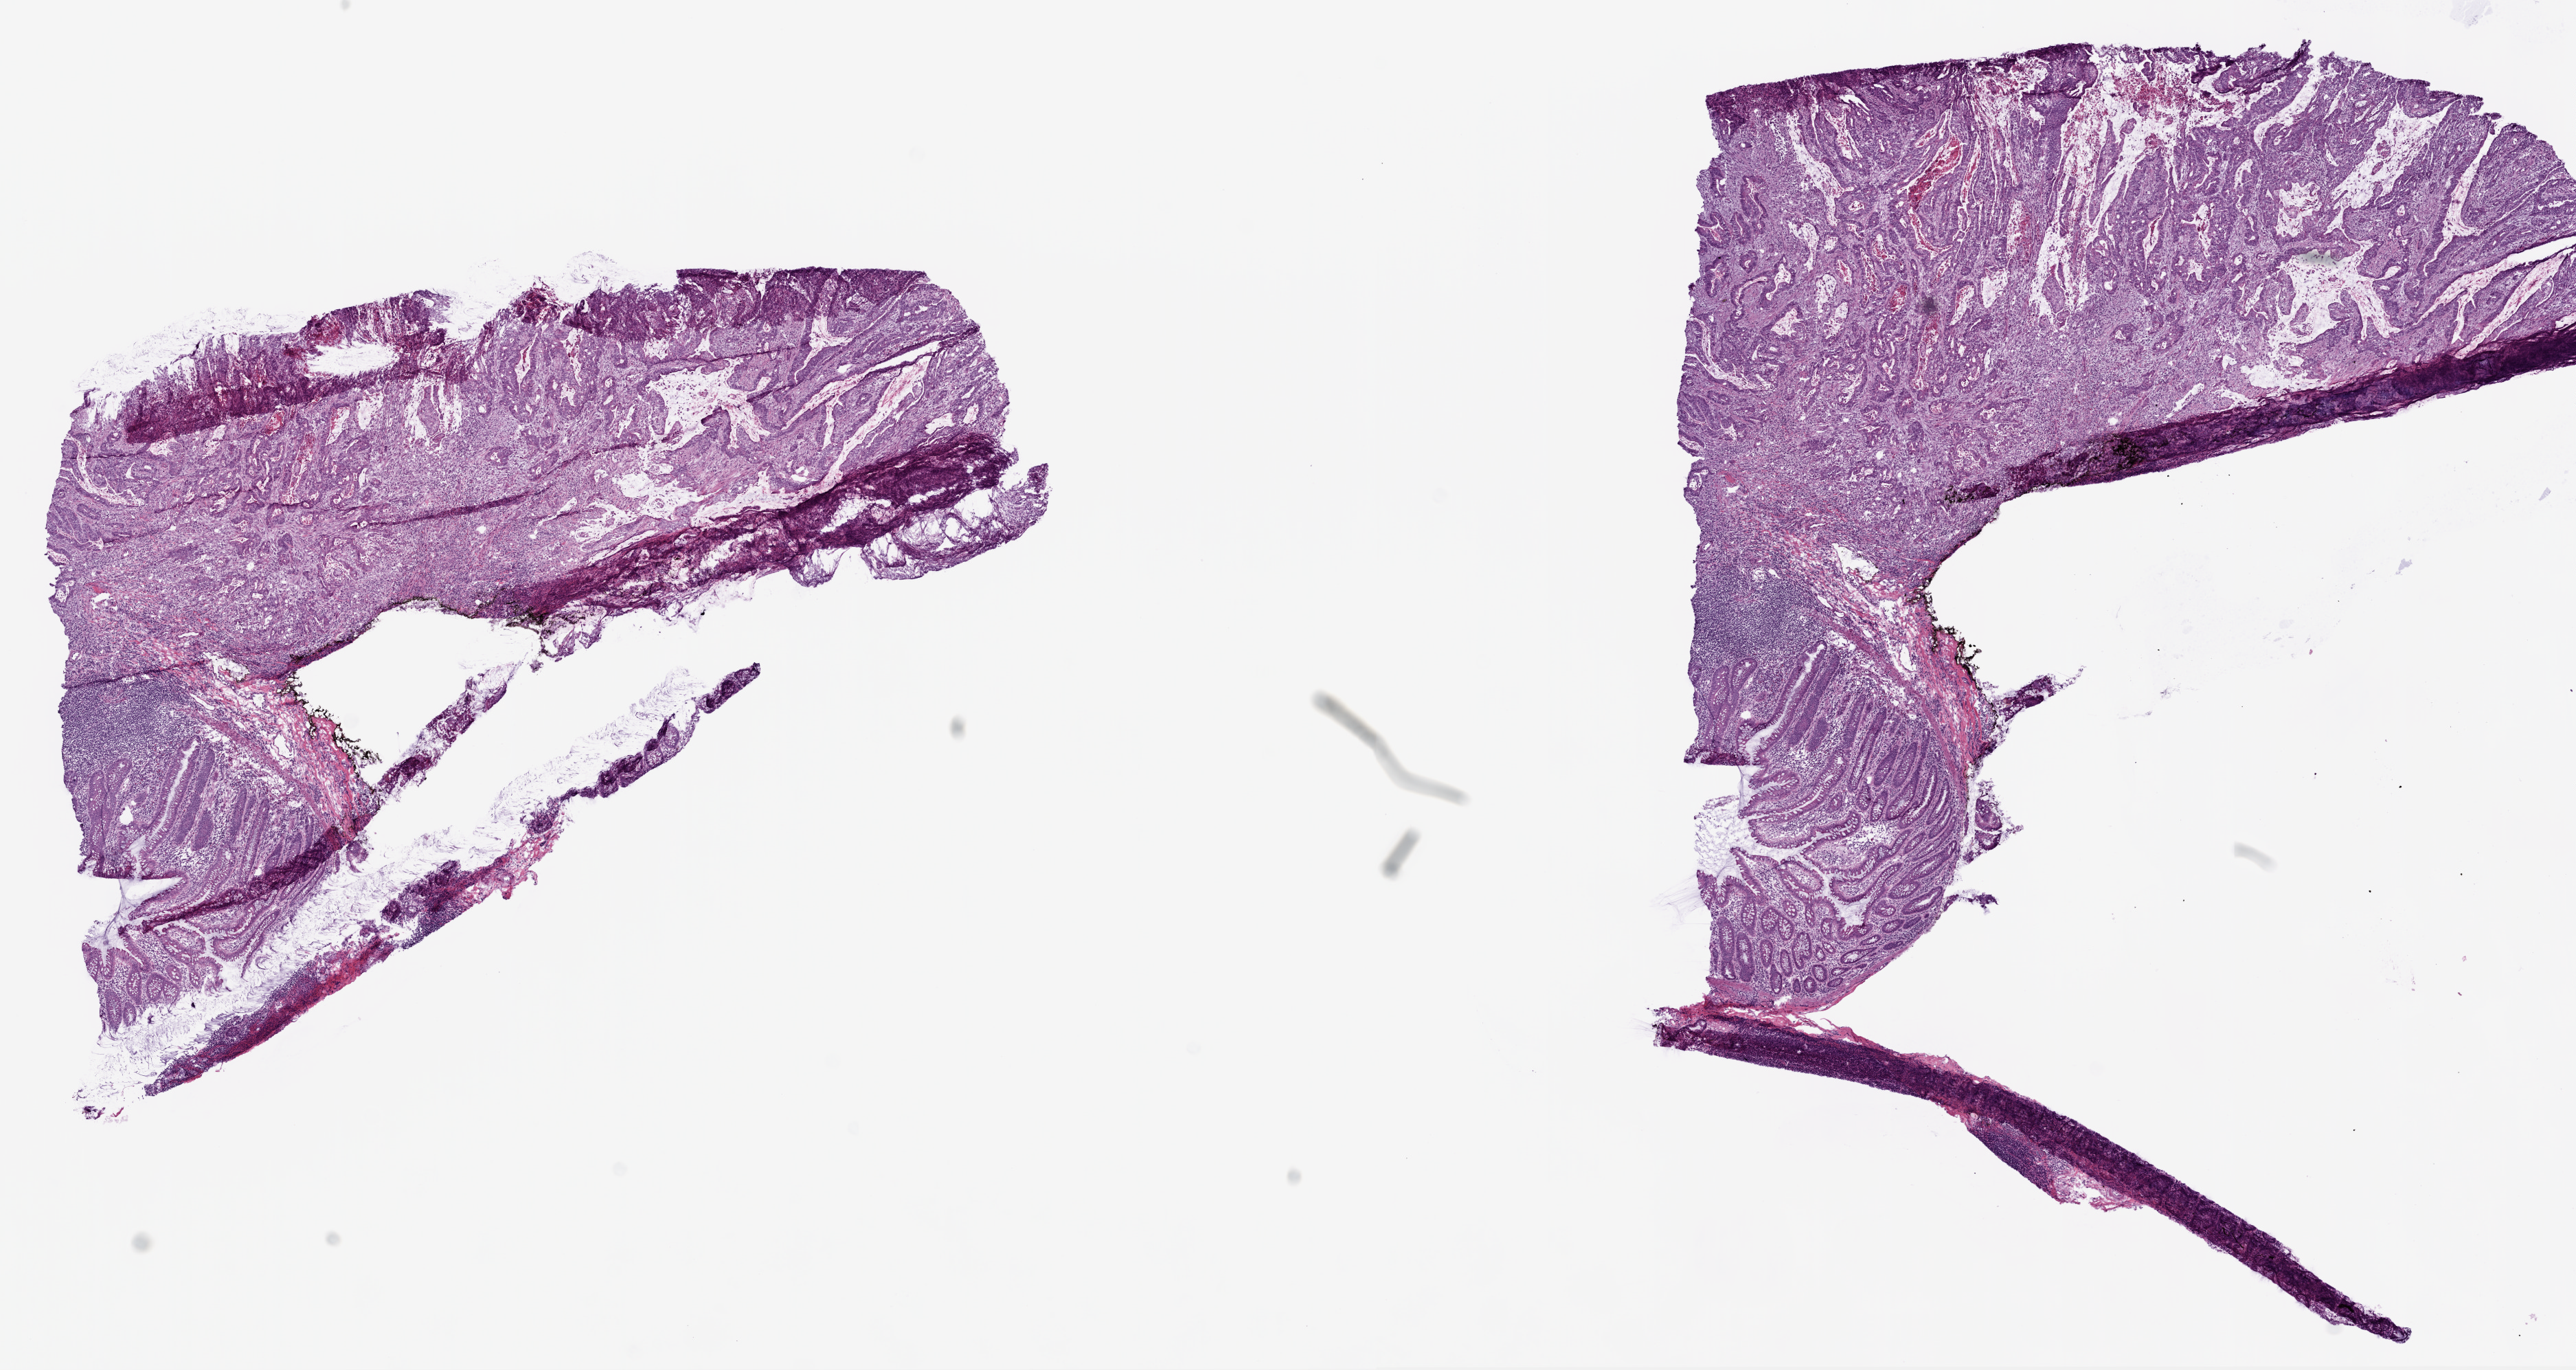
Digitized H&E tissue section (whole slide), a low-resolution overview of the entire scanned area, about 15.0 x 8.0 mm (acquisition: 20x scan). Frozen section from the bottom of the tissue portion. Colon, primary tumour sample. Patient: female, age at initial diagnosis 80 years. Slide review estimates, as recorded: tumour cells 70%, tumour nuclei 64%, normal cells 20%, stromal cells 0%, necrosis 10%. Infiltration values recorded for this section: lymphocyte infiltration 10%, monocyte infiltration 1%, neutrophil infiltration 13%.
* AJCC pathologic stage: IIA
* diagnosis: Adenocarcinoma, NOS (ascending colon)